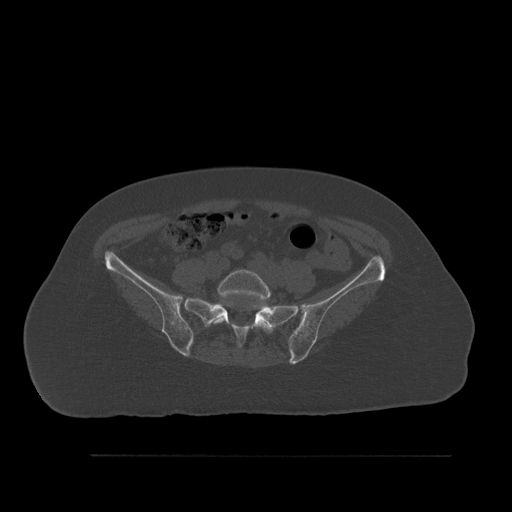
CT including the spine, one axial slice. Position 180 of 527 along the scan axis. Bone window (W 1800 / L 400 HU). 1.5 mm slice thickness. 512 × 512 image matrix, field of view 470 × 470 mm. Female patient, age 73 years. Case-level facts recorded for this patient, not image findings: primary cancer: breast.
Annotated regions visible in this slice (semi-automatic segmentation, software-assisted and operator-edited):
- L5 vertebra: bounding box [x1, y1, x2, y2] px = [211, 269, 273, 334]